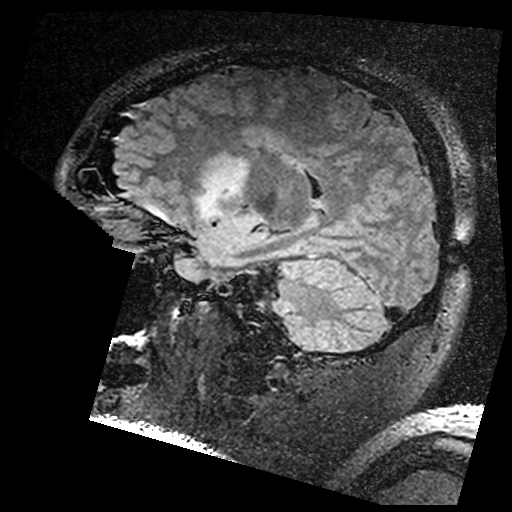
Brain MRI from a brain-tumour surgery series, one sagittal slice. Position 110 of 176 along the scan axis. T2 FLAIR. 1 mm slice thickness. 512 × 512 image matrix, field of view 250 × 250 mm. From the clinical record (not read from this slice): histopathology: Astrocytoma; WHO grade: 3; IDH mutation: yes; tumour location: Left Insular.
Annotated regions visible in this slice (manually delineated by an expert):
- residual tumour: box from (x=208, y=151) to (x=250, y=202) px